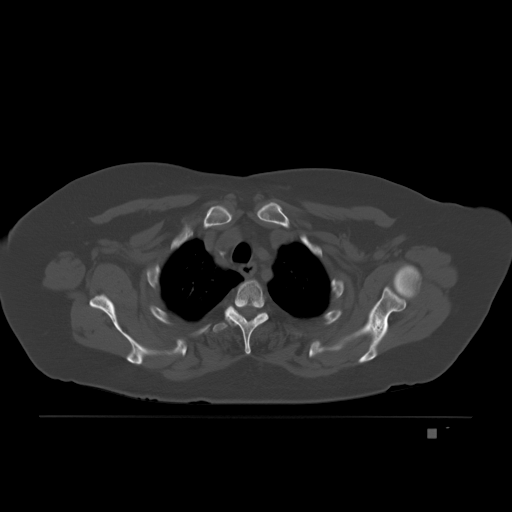
CT including the spine, one axial slice. Slice 165 of 221 in the series (ordered by position). Bone window (W 1800 / L 400 HU). 512 × 512 image matrix. Patient: female, 63 years. From the clinical record (not read from this slice): primary cancer: breast.
Outlined on this slice (semi-automatic segmentation, software-assisted and operator-edited):
- T3 vertebra: bounding box <216,311,268,331> (left, top, right, bottom; pixels)